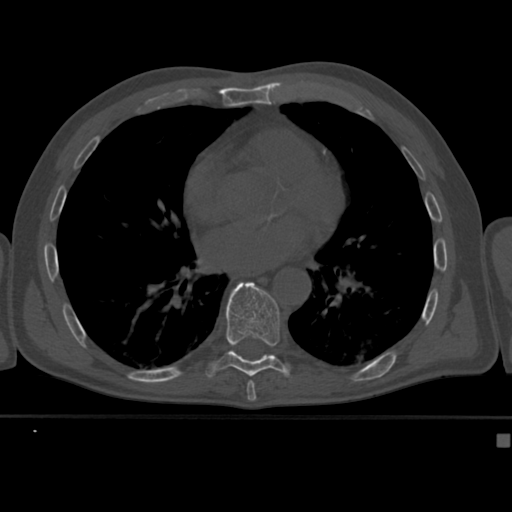
CT including the spine, one axial slice. Reconstruction kernel Br40s. 120 kVp. Bone window (W 1800 / L 400 HU). 1.5 mm slice thickness. 512 × 512 image matrix. Patient: male, 64 years. From the clinical record (not read from this slice): primary cancer: uterus; vertebrae with lytic lesions (as recorded): T1, T4, T5, T7, L5.
Structures marked on this image (semi-automatic segmentation, software-assisted and operator-edited):
- T8 vertebra: bounding box [x1, y1, x2, y2] px = [250, 380, 252, 382]
- T9 vertebra: [205, 281, 293, 378]